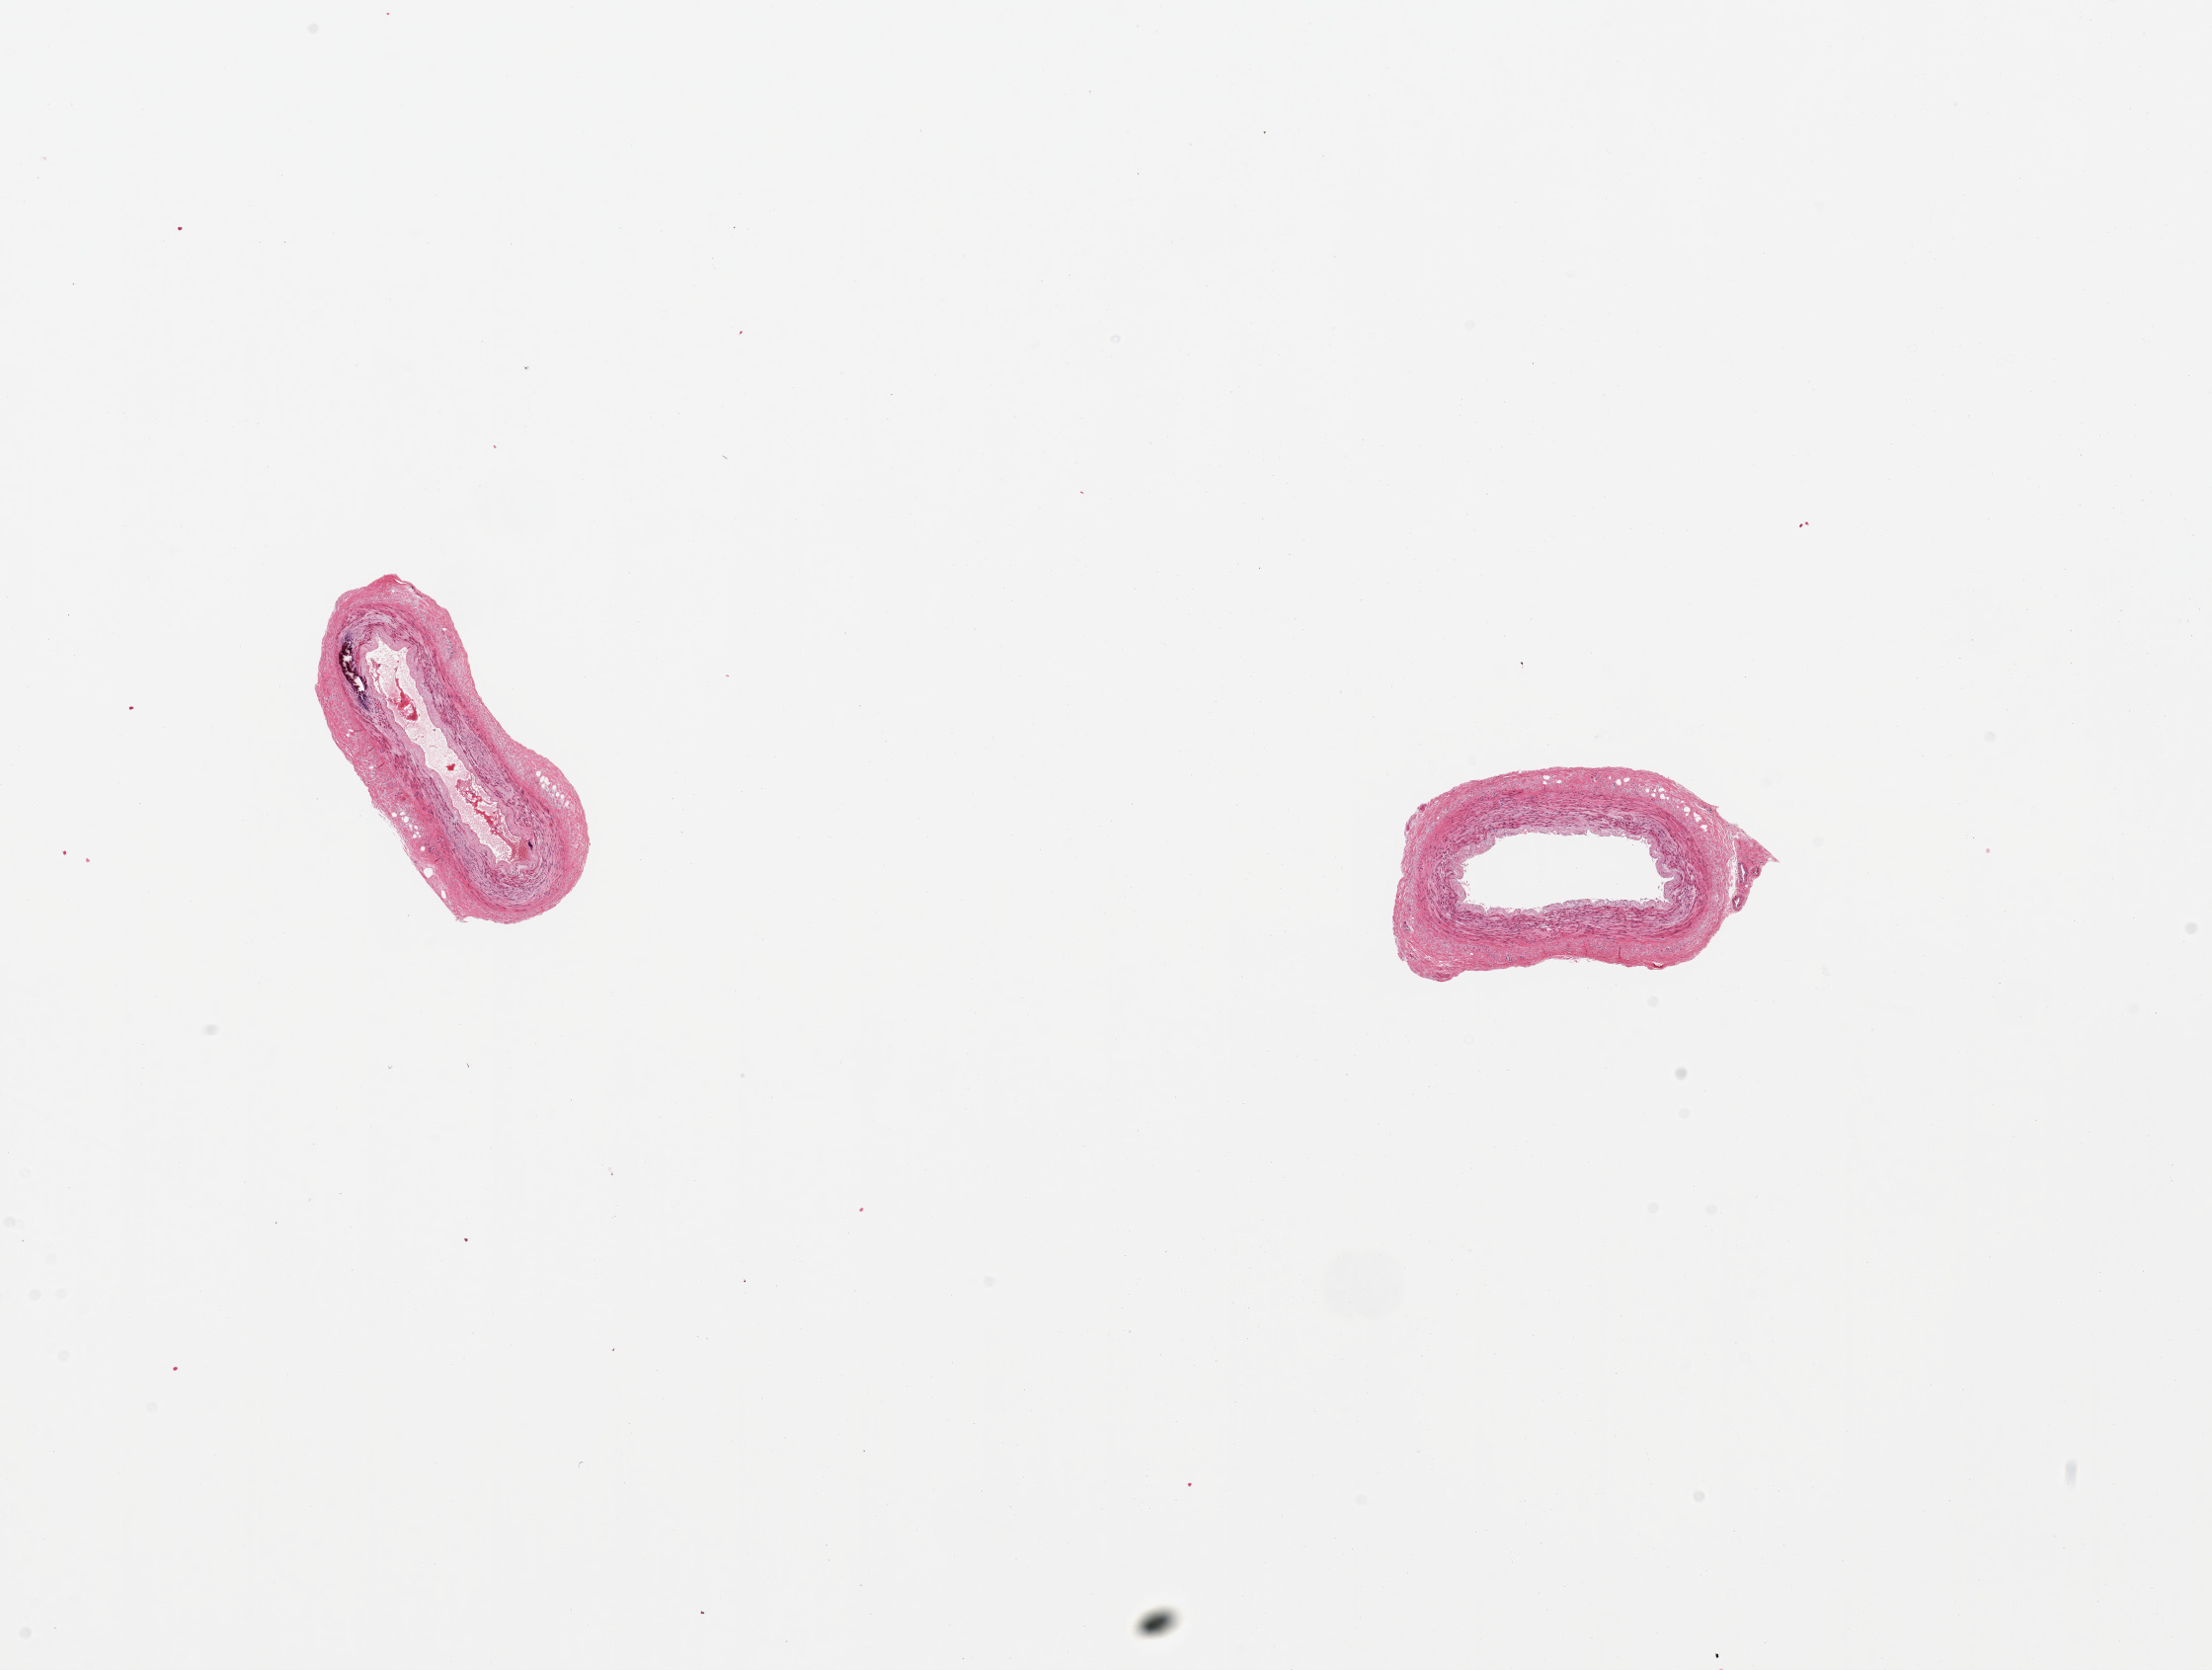
Whole-slide image, haematoxylin and eosin stain, a low-resolution overview of the entire scanned area, about 17.7 x 13.4 mm; PAXgene-fixed, paraffin-embedded tissue; section of tibial artery (target tissue); donor tissue sample.
Review note (as recorded): 2 pieces; 1 mm mural calcification; no plaques; well trimmed.